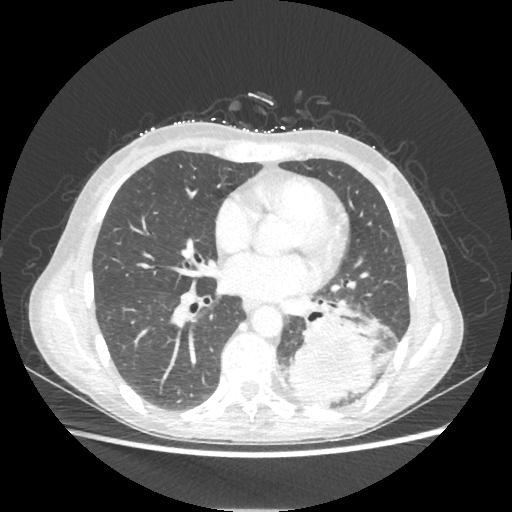
Chest CT, one axial slice; reconstruction kernel STANDARD; 80 kVp; lung window (W 1500 / L -600 HU); 1.25 mm slice thickness; 512 × 512 image matrix, field of view 360 × 360 mm. Female patient, age 53 years. From the clinical record (not read from this slice): clinical TNM (as recorded): T3 N0 M0.
Annotated regions visible in this slice (bounding box drawn by a radiologist):
- lung tumour (recorded histology: adenocarcinoma): bounding box (x1, y1, x2, y2) in pixels: (290, 311, 379, 401)